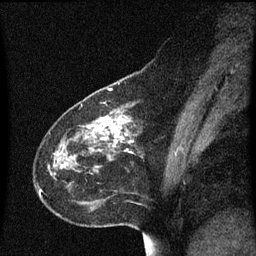
Breast MRI (dynamic contrast-enhanced), one sagittal slice; dynamic contrast-enhanced series, image 2 of 3 at this slice position (ordered by acquisition); 1.5 T; TE 4.2 ms, TR 8.4 ms; 2 mm slice thickness; 256 × 256 image matrix, field of view 200 × 200 mm. Female patient, age 49 years. Case-level facts recorded for this patient, not image findings: setting: breast cancer imaged before/during neoadjuvant chemotherapy; receptor status: HR-positive, HER2-negative.
Structures marked on this image (semi-automatic segmentation, software-assisted and operator-edited):
- analysis volume of interest (the breast-tissue region the enhancement analysis was run in; not a lesion): box from (x=37, y=96) to (x=145, y=215) px
- tumour enhancement mask (voxels above the 70 % enhancement threshold inside the analysis volume of interest): (x=98, y=118)–(x=126, y=143)